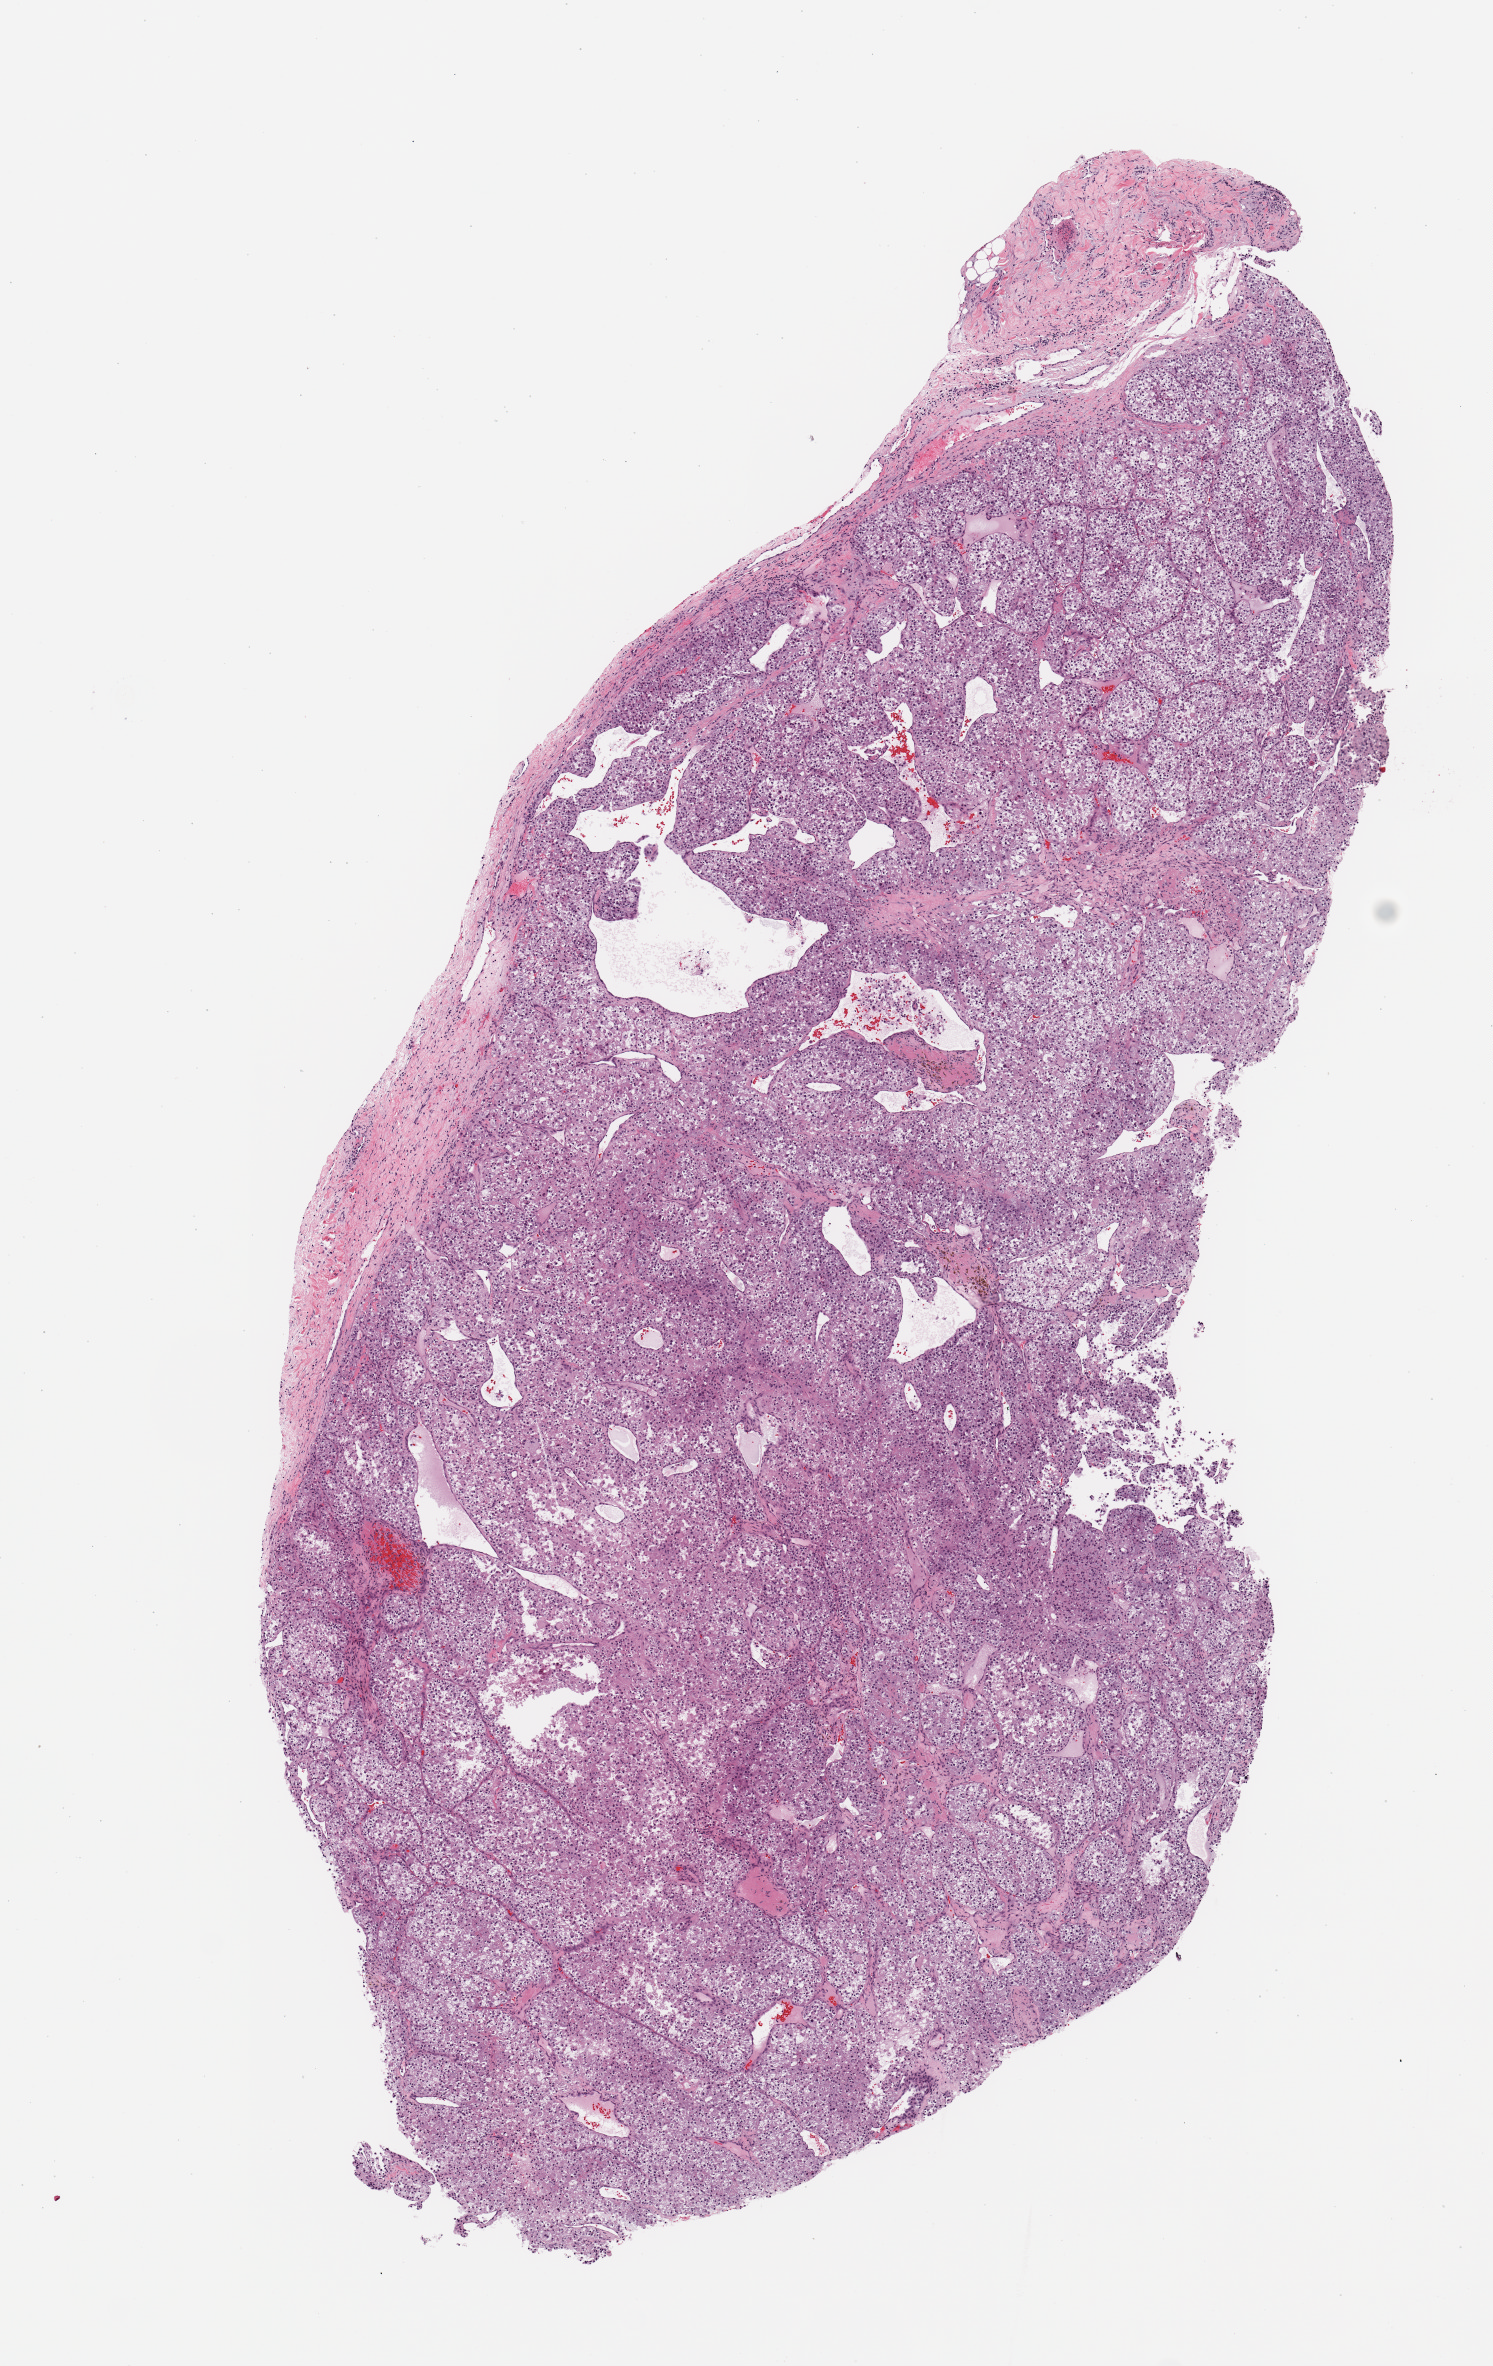
Hematoxylin and eosin (H&E) stained whole-slide image — whole scanned area (about 5.9 x 9.4 mm, slide scanned at 20x) shown as a low-resolution overview. Tumour tissue sample, sampled site: kidney. Patient: female, age 63 years. Histologic grade: G4 (undifferentiated). Slide review estimates, as recorded: tumour nuclei 90%, necrosis 5%.
• diagnosis: Renal cell carcinoma, NOS
• AJCC pathologic stage: IV